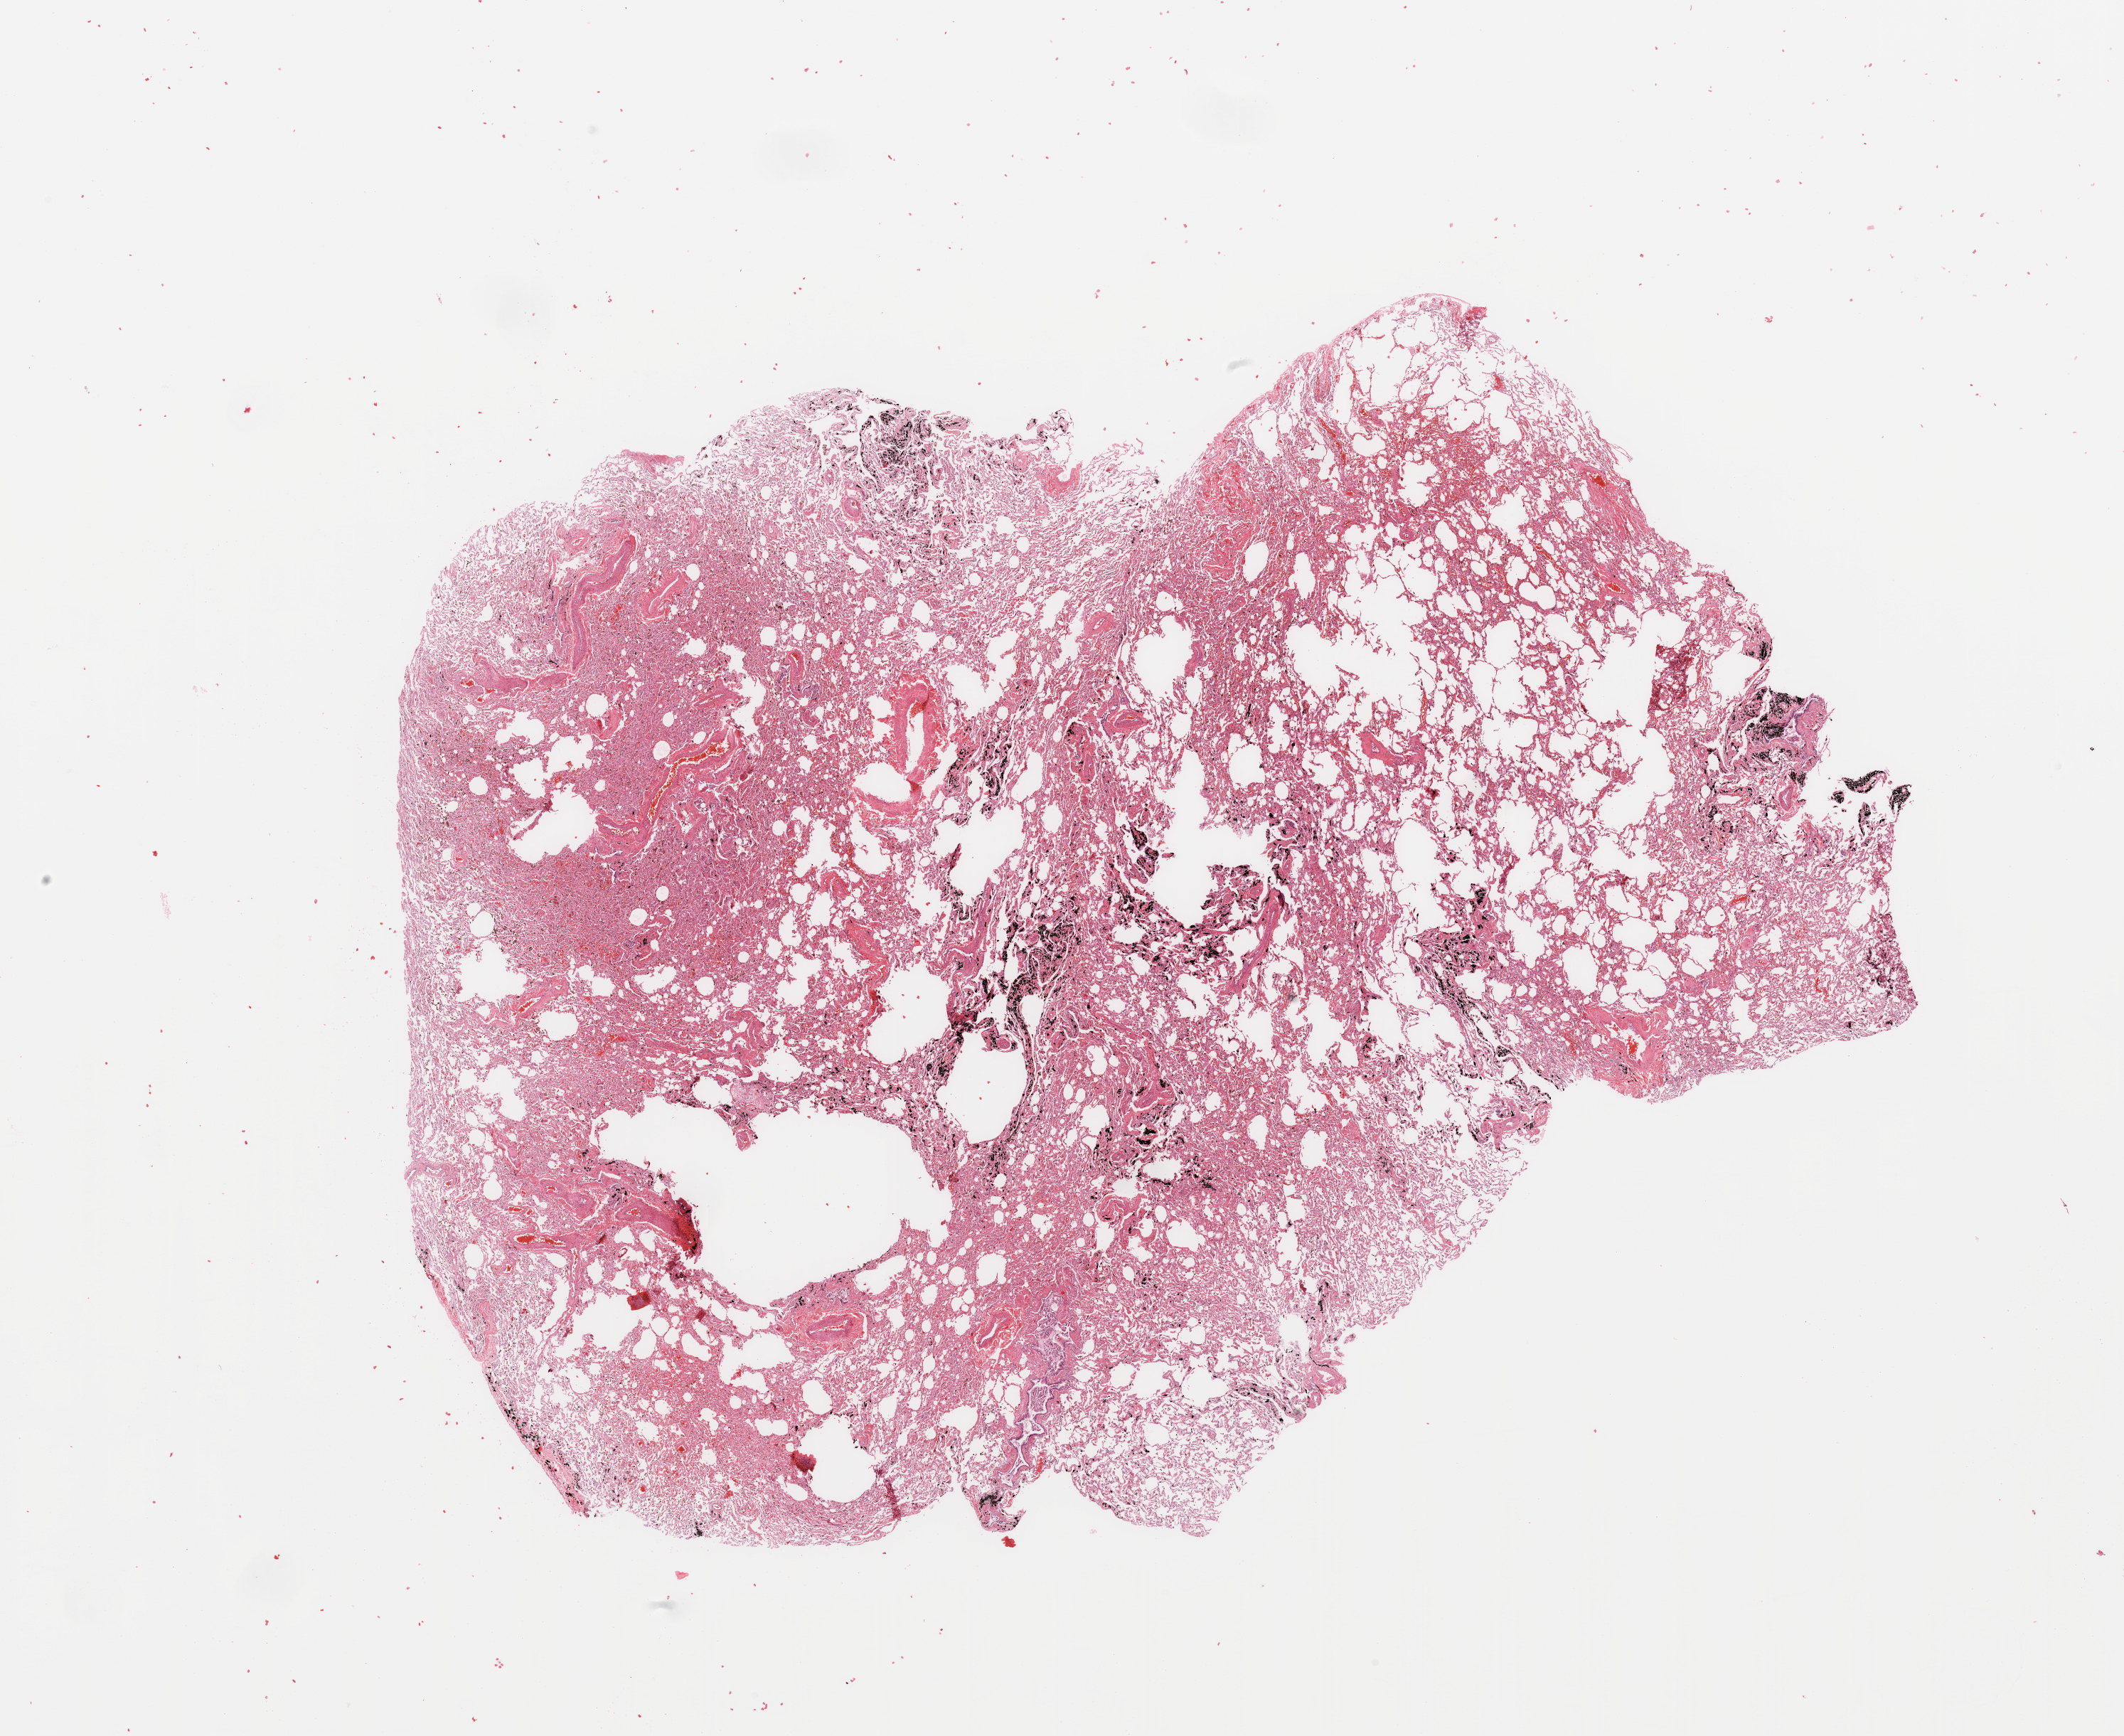
H&E whole-slide image, low-resolution overview of the scanned area, about 23.6 x 19.3 mm (from a 20x scan). Lung, normal (non-tumour) tissue. Patient: male, age 54 years.
This section: normal (non-tumour) tissue from the same patient. Patient diagnosis: Adenocarcinoma, NOS.